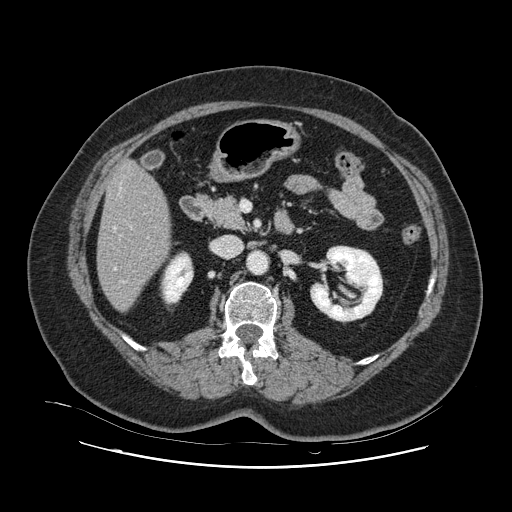
Contrast-enhanced abdominal CT, one axial slice. Position 39 of 132 along the scan axis. 120 kVp. Soft-tissue window (W 400 / L 40 HU). 2.5 mm slice thickness. 512 × 512 image matrix, field of view 391 × 391 mm. Female patient, age 73 years. Case-level facts recorded for this patient, not image findings: diagnosis: colorectal cancer liver metastases, imaged before liver resection; multiple liver metastases: no; largest metastasis: 7 cm; disease in both lobes: no.
Annotated regions visible in this slice (manually delineated by an expert):
- hepatic veins: bounding box (x1, y1, x2, y2) in pixels: (114, 189, 121, 270)
- liver: (98, 162, 169, 311)
- planned liver remnant (the part of the liver to remain after resection): (98, 162, 169, 311)
- portal vein (with intrahepatic branches): (123, 227, 132, 283)